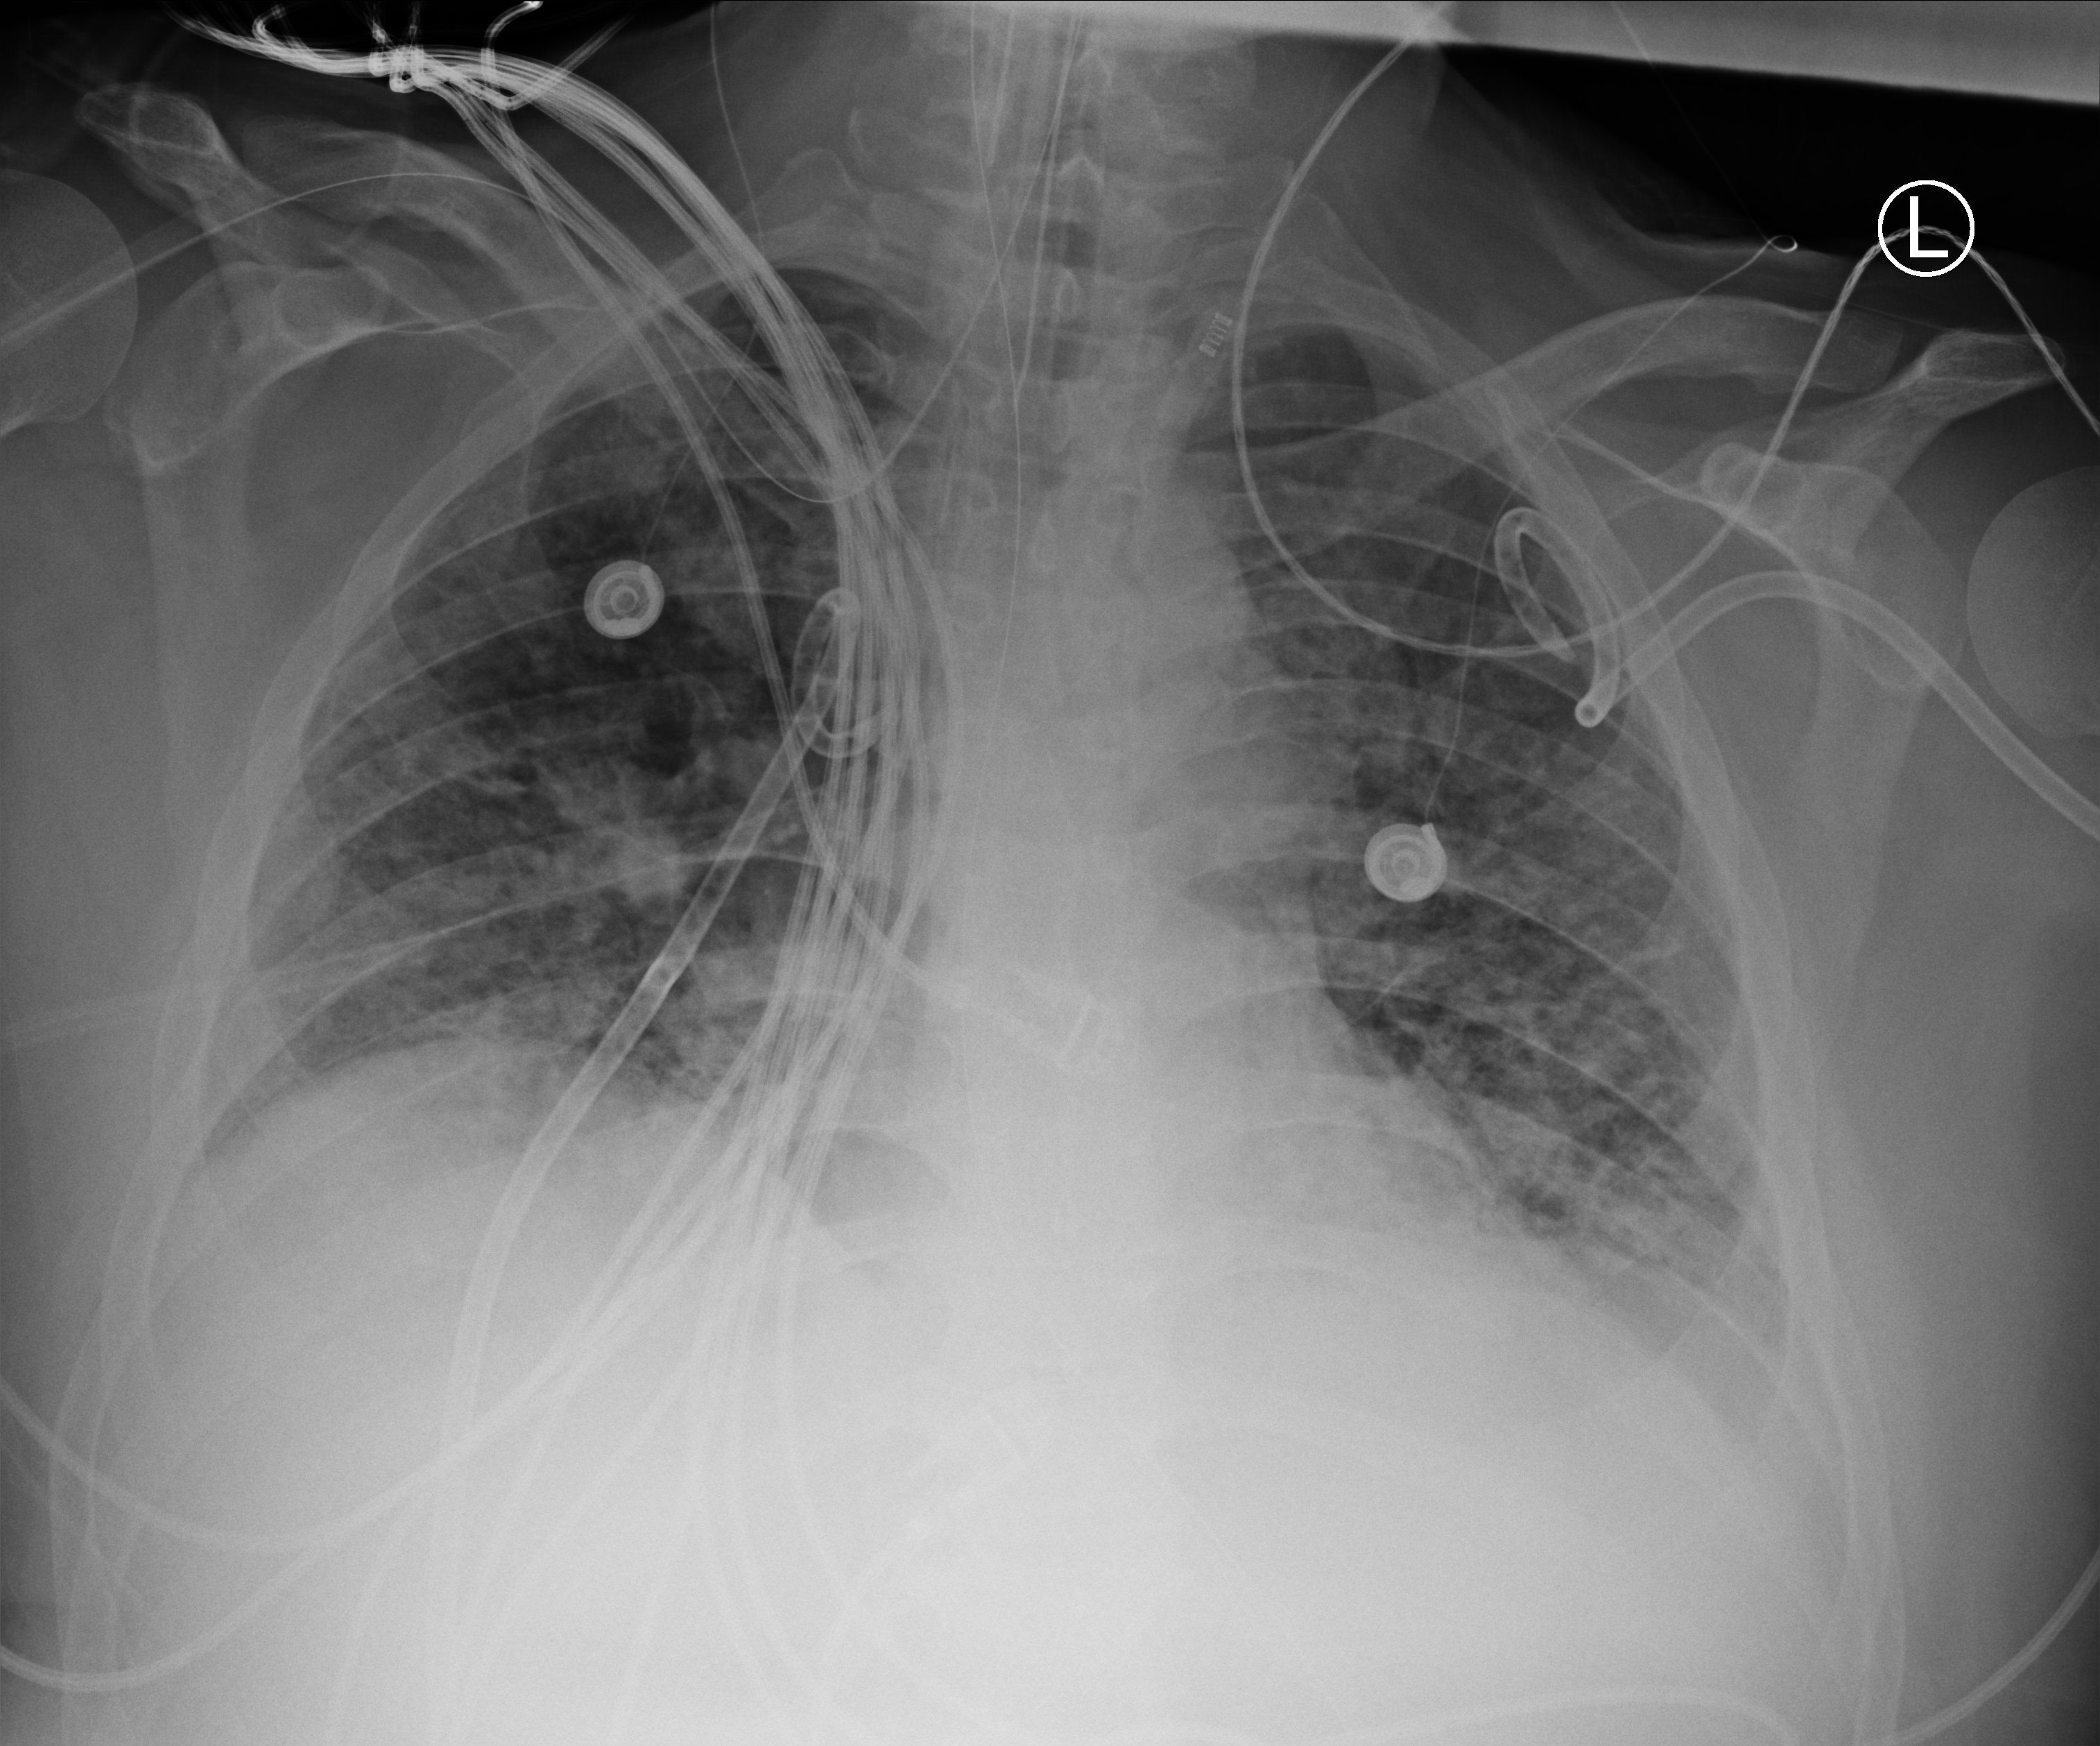
Bedside chest radiograph (computed radiography), anteroposterior (AP) projection. Patient hospitalised with COVID-19, aged 18–59 years.
Hospital-stay facts (about this admission, not read from this image; timing relative to this image not recorded): admitted to intensive care during this hospital stay: yes.